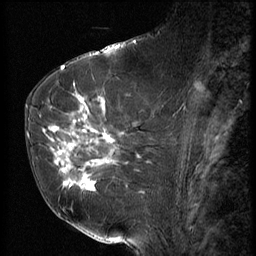
Breast MRI (dynamic contrast-enhanced), one sagittal slice; slice 30 of 56 in the series (ordered by position); 3 images stored at this slice position (order not interpretable as contrast timing); 1.5 T; TE 4.2 ms, TR 9 ms; 256 × 256 image matrix, field of view 180 × 180 mm. Female patient, age 61 years. Case-level facts recorded for this patient, not image findings: setting: breast cancer imaged before/during neoadjuvant chemotherapy; receptor status: HR-positive, HER2-negative.
Structures marked on this image (semi-automatically segmented with operator editing):
- analysis volume of interest (the breast-tissue region the enhancement analysis was run in; not a lesion): bounding box [x1, y1, x2, y2] px = [47, 89, 153, 191]
- tumour enhancement mask (voxels above the 140 % enhancement threshold inside the analysis volume of interest): [48, 93, 116, 190]